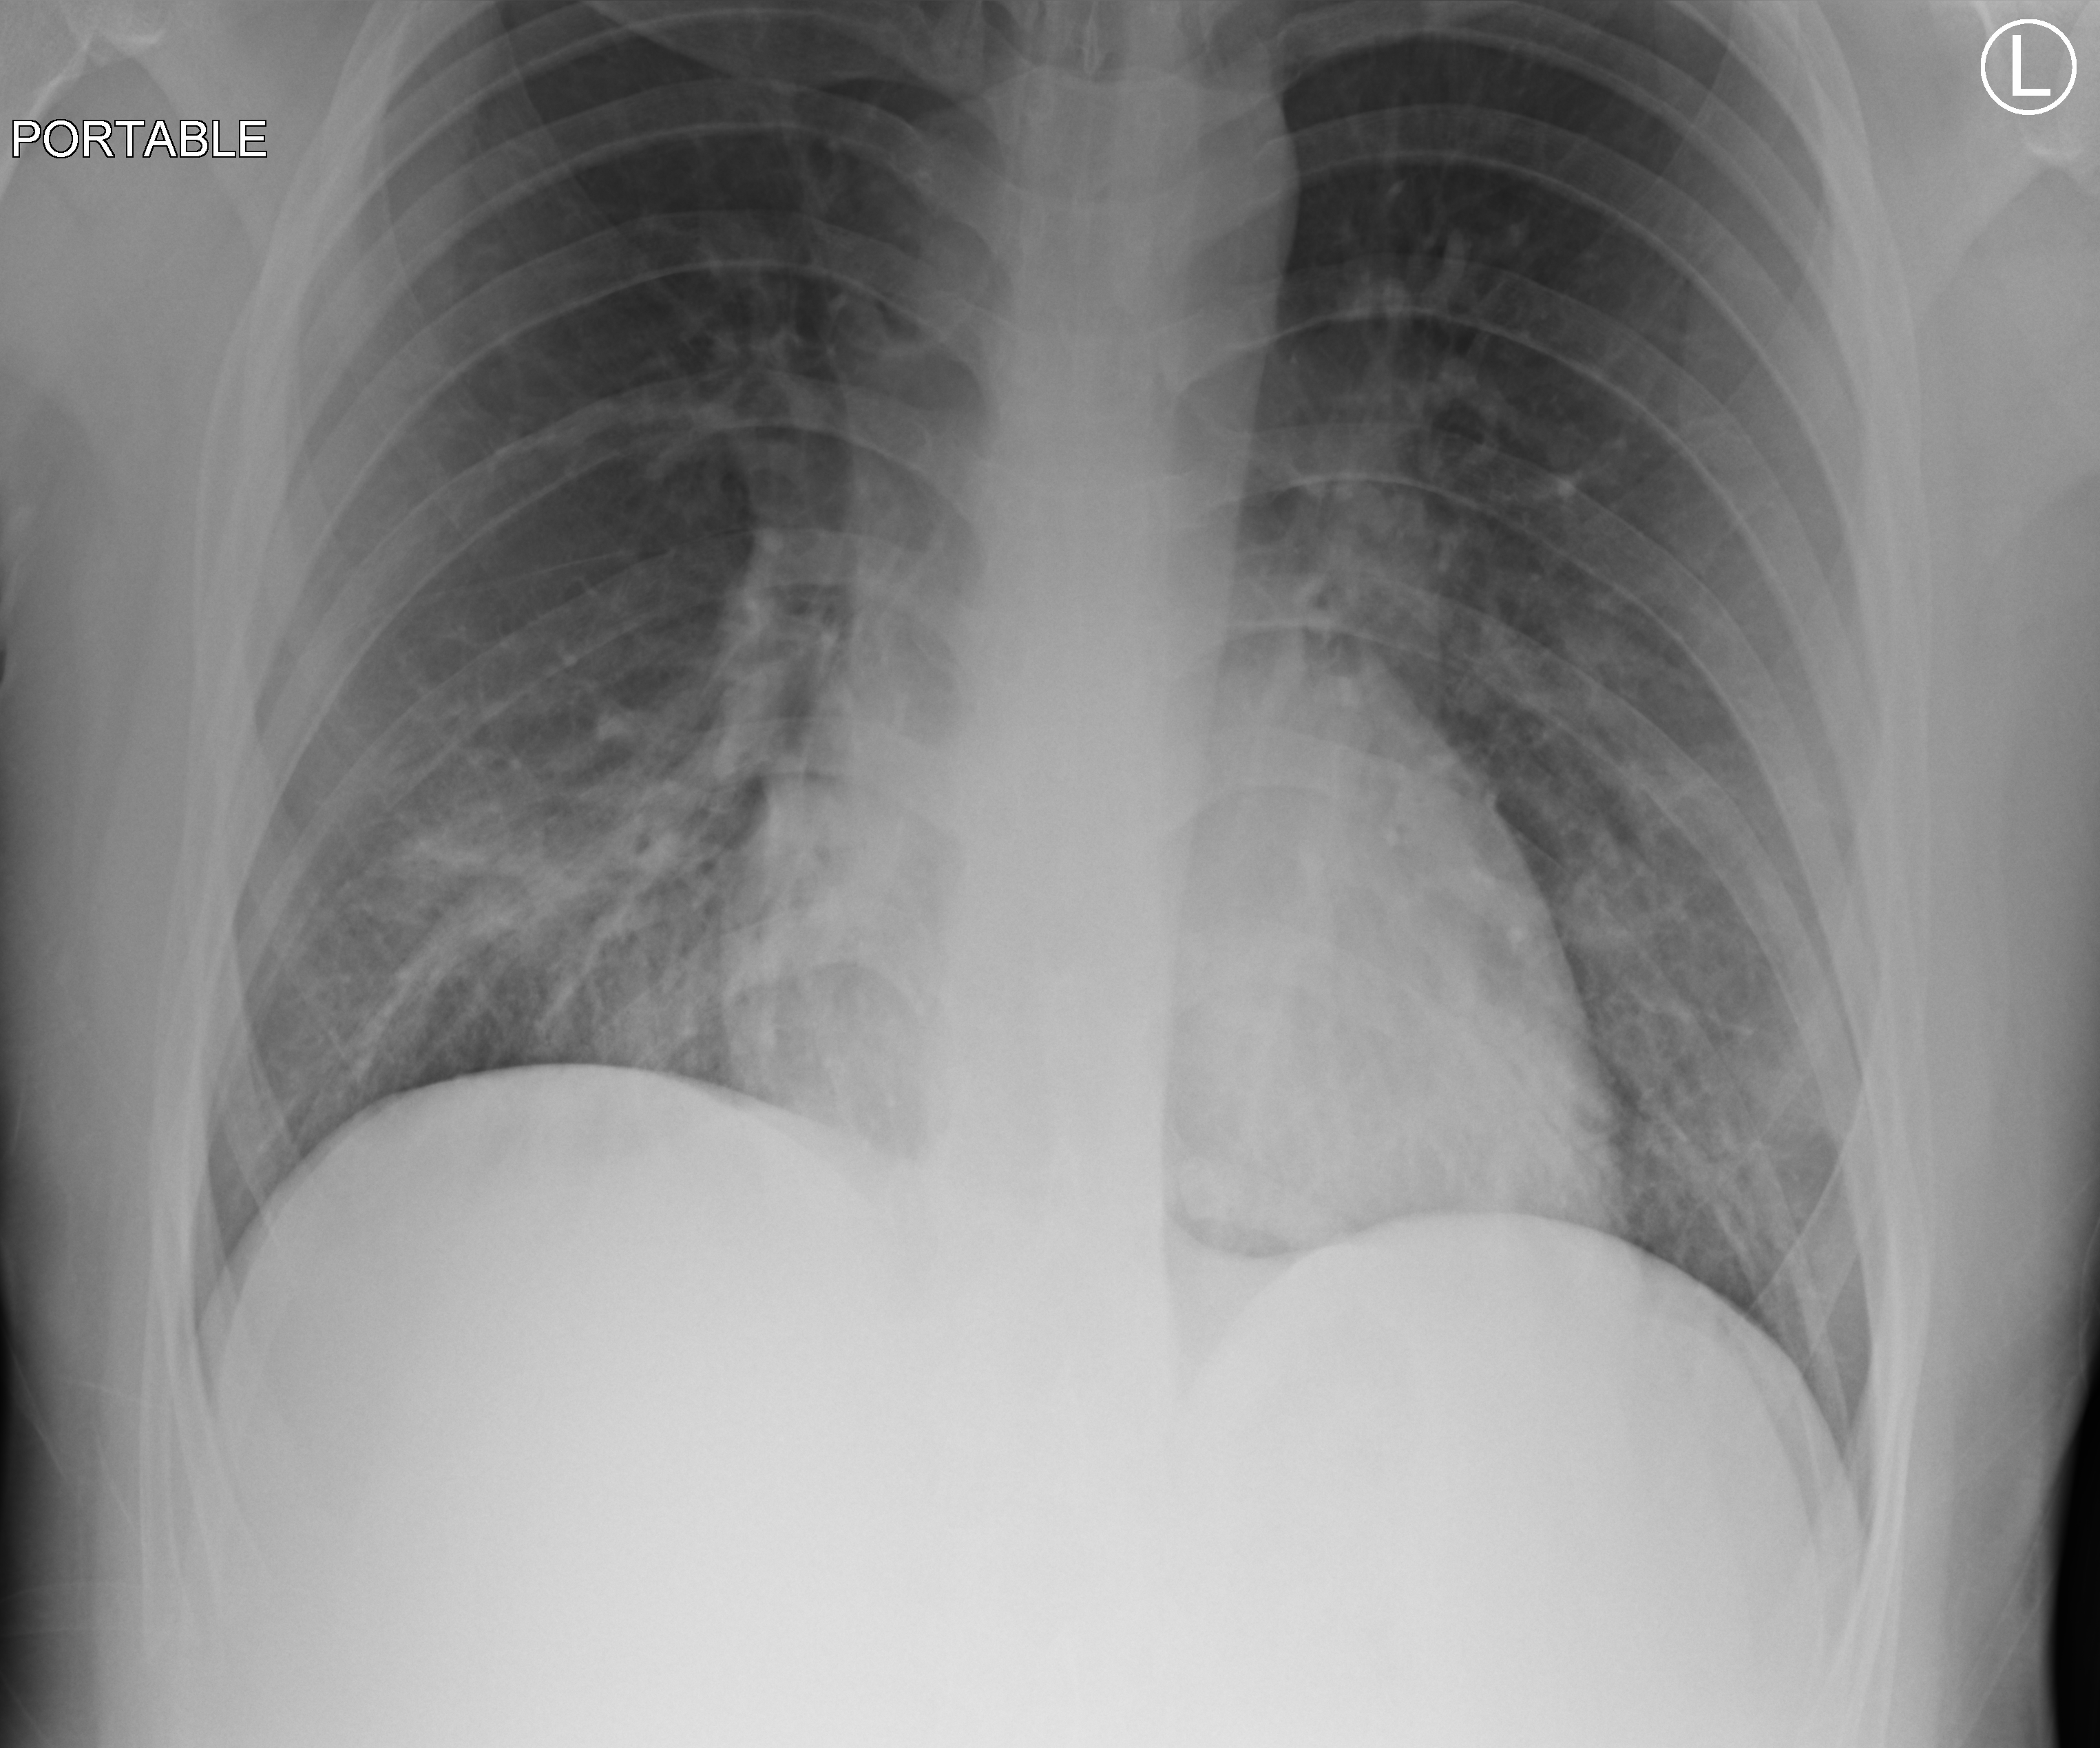
Chest X-ray (portable), anteroposterior (AP) projection. Male patient hospitalised with COVID-19, age 18–59 years.
Hospital-stay facts (about this admission, not read from this image; timing relative to this image not recorded):
- length of hospital stay: 6 days